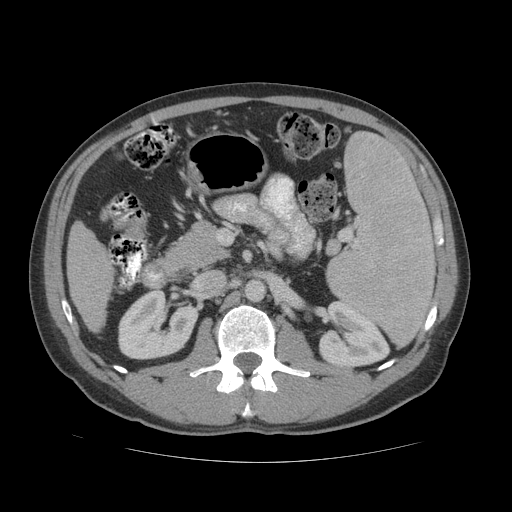
Contrast-enhanced abdominal CT (liver protocol), one axial slice. 140 kVp. Soft-tissue window (W 400 / L 40 HU). 2.5 mm slice thickness. 512 × 512 image matrix, field of view 400 × 400 mm. Case-level facts recorded for this patient, not image findings: diagnosis: hepatocellular carcinoma (patient treated with transarterial chemoembolisation; whether this scan precedes or follows treatment is not stated here); TNM stage (as recorded): Stage-IVB; Child-Pugh class: B; tumour differentiation: well differentiated; tumour nodularity: multinodular.
Annotated regions visible in this slice (semi-automatic segmentation, software-assisted and operator-edited):
- liver parenchyma outside the tumour (the mass and vessels are separate outlines, so this box may not span the whole liver): box from (x=66, y=222) to (x=114, y=331) px